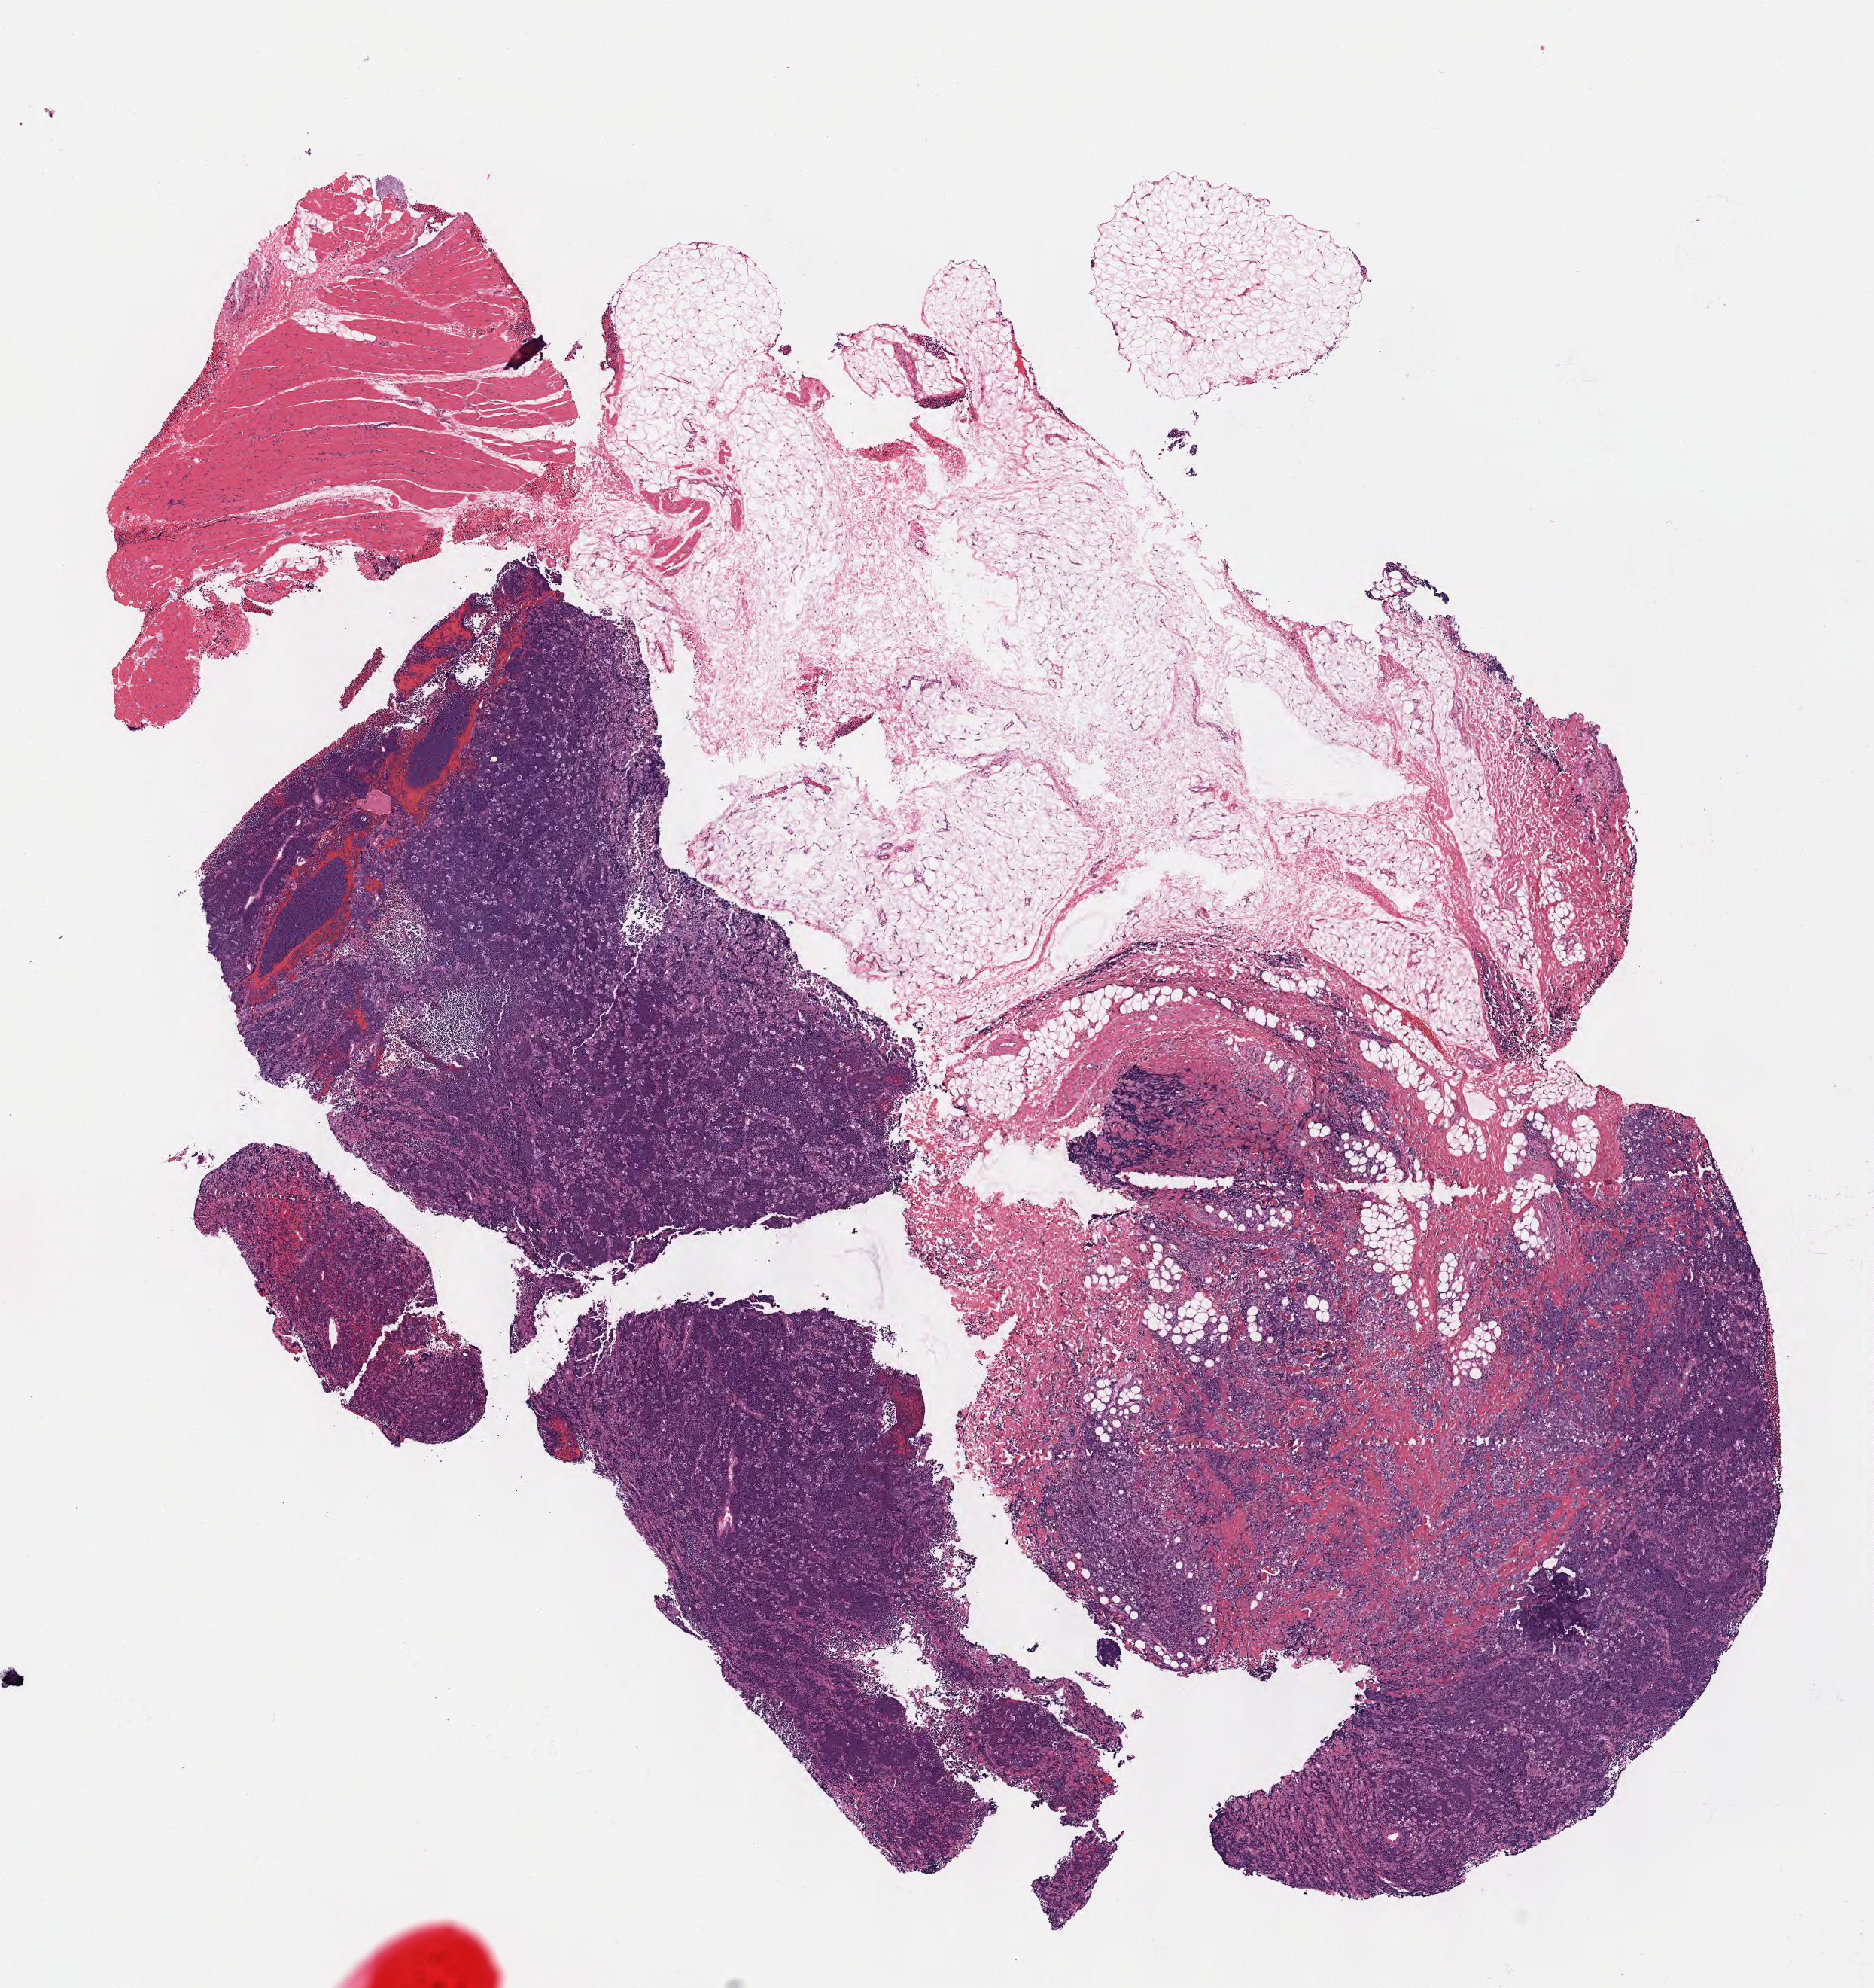
Haematoxylin and eosin whole-slide image — a low-resolution overview of the entire scanned area, about 10.1 x 10.7 mm, specimen: tumor tissue, site: head and neck. Patient: male, age at initial diagnosis 4 years.
Histologic diagnosis: Burkitt lymphoma, NOS.